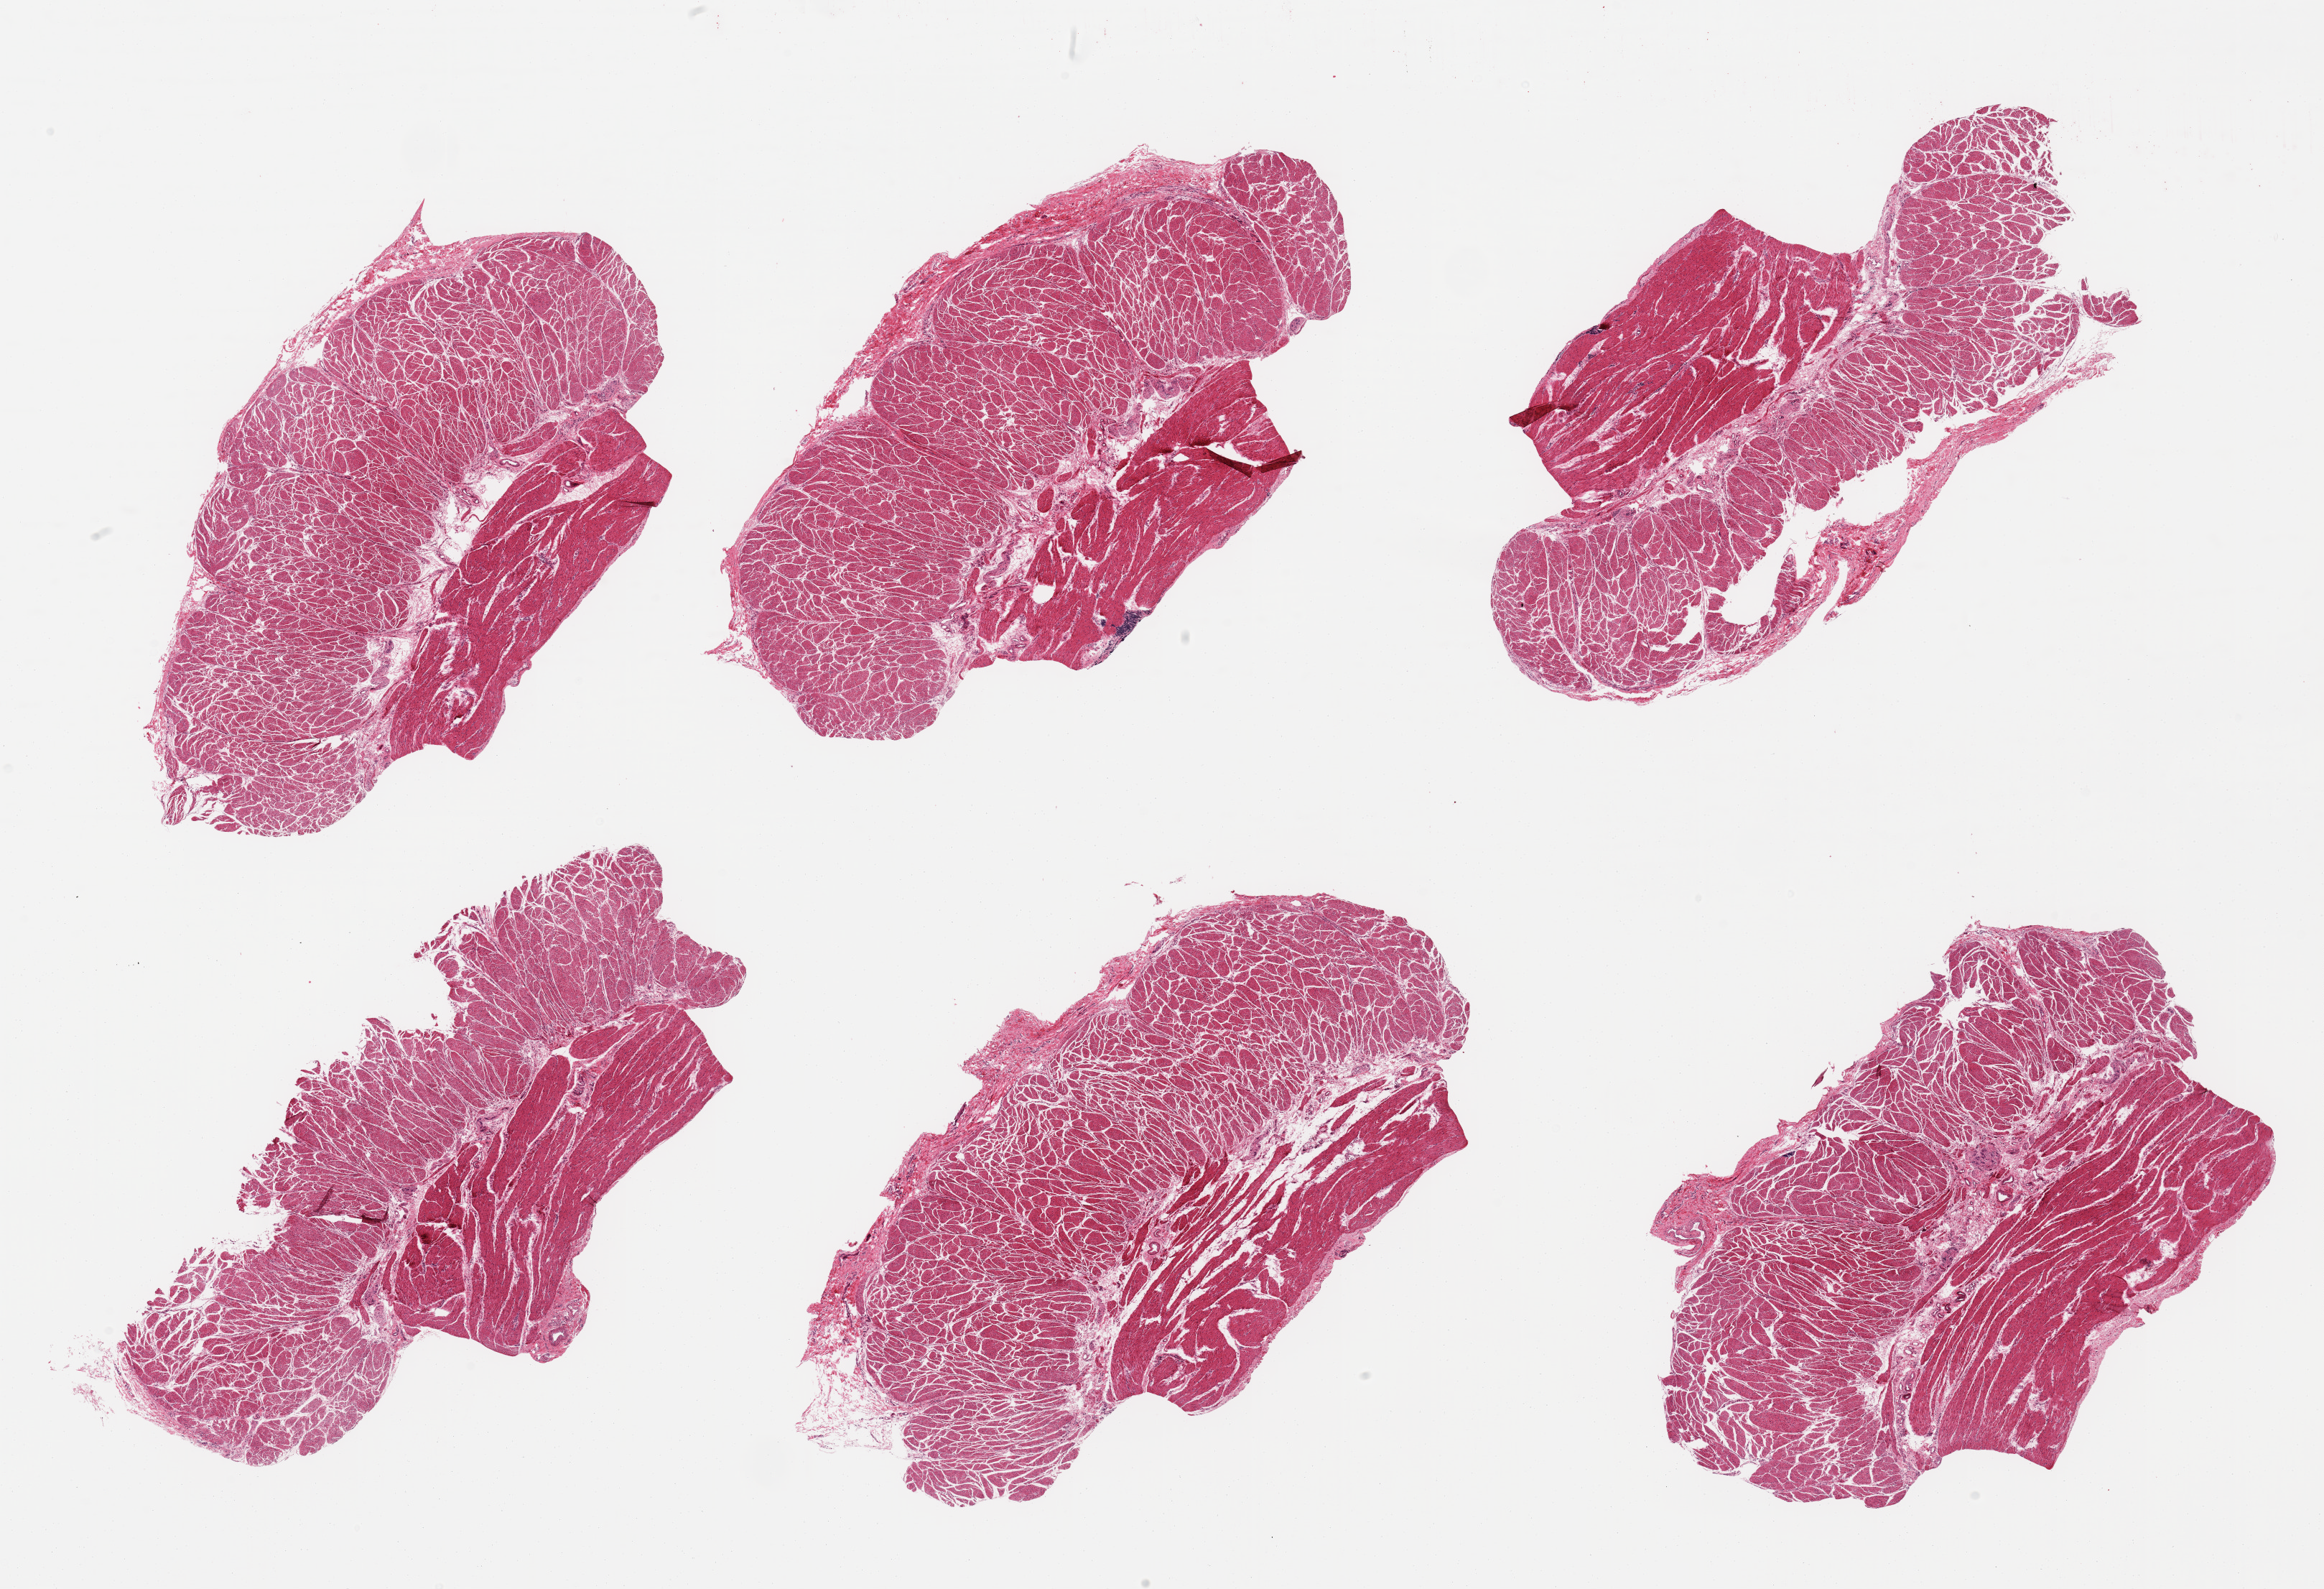
Digitized H&E-stained section — low-resolution overview of the scanned area, about 25.6 x 17.5 mm, PAXgene-fixed, paraffin-embedded tissue, section of esophageal muscle (target tissue), donor tissue sample. Donor: male.
Review note (as recorded): 6 pieces; well trimmed, focal collections of lymphocytes.